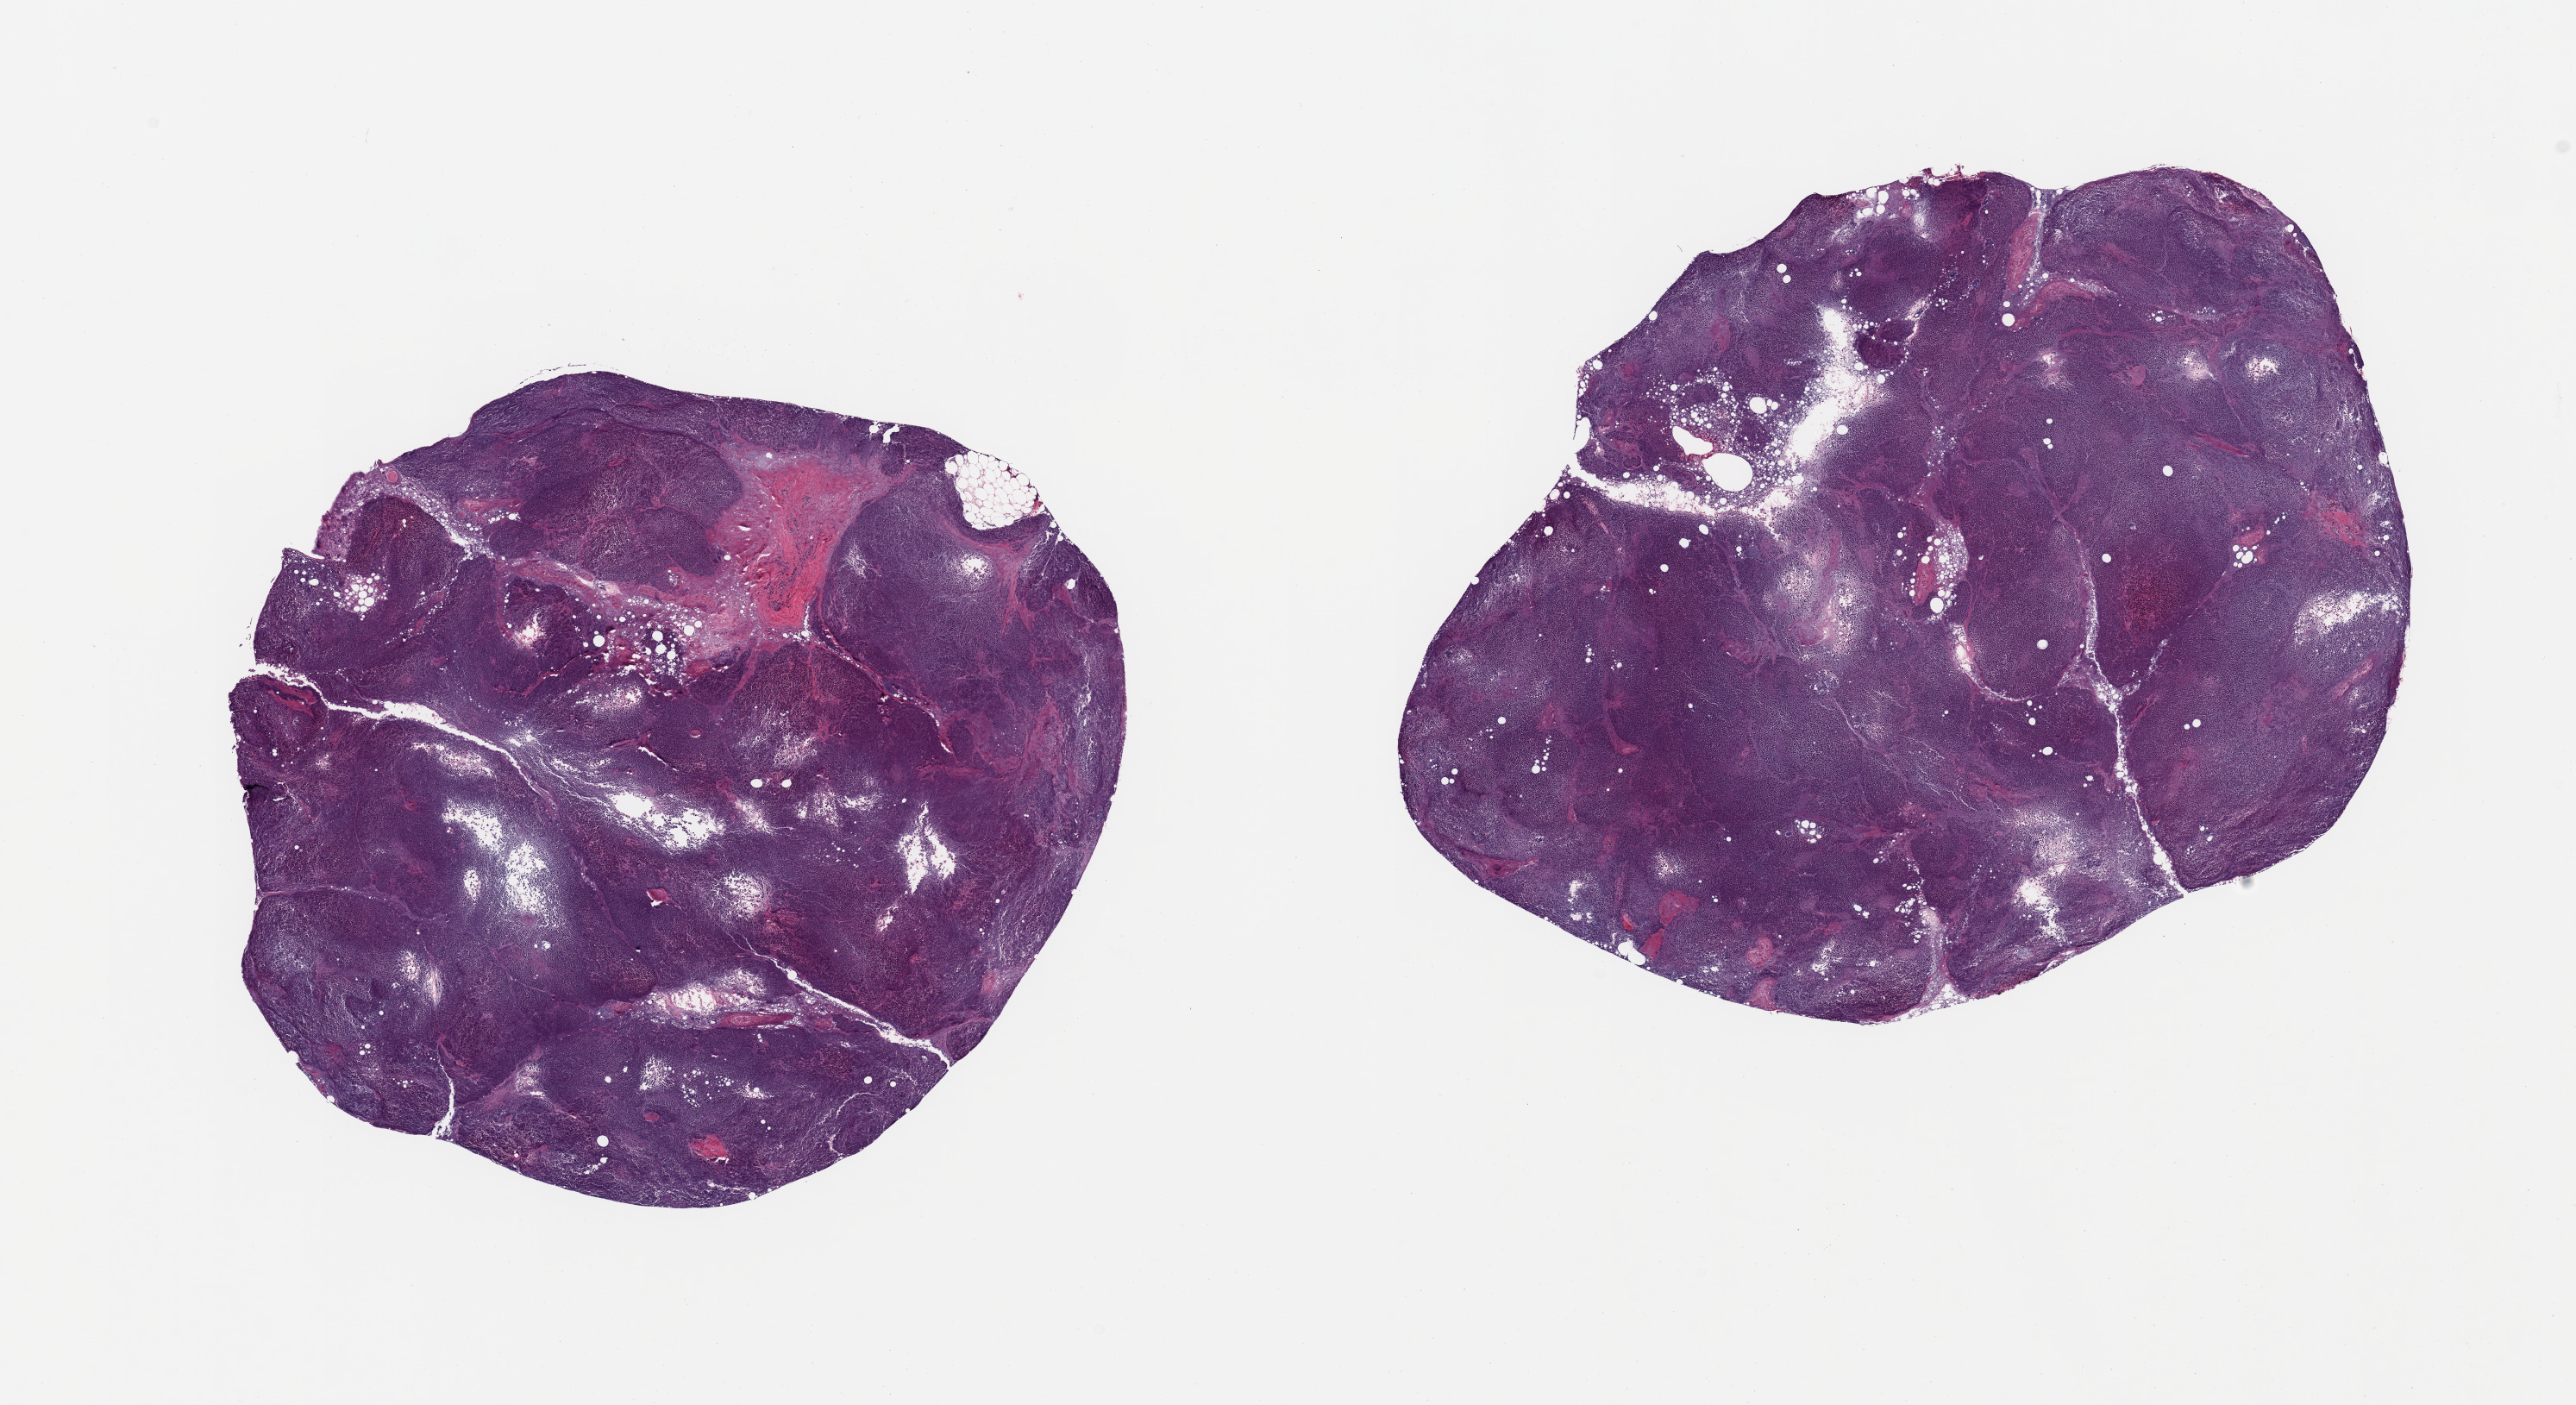
Digitized hematoxylin and eosin (H&E)-stained section — a low-resolution overview of the entire scanned area, about 23.6 x 12.9 mm (slide scanned at 20x), PAXgene-fixed, paraffin-embedded tissue, sampled site (target tissue): adrenal gland, donor tissue sample. Donor: male.
- review note (as recorded): 2 pieces; severely autolyzed pancreas, not adrenal